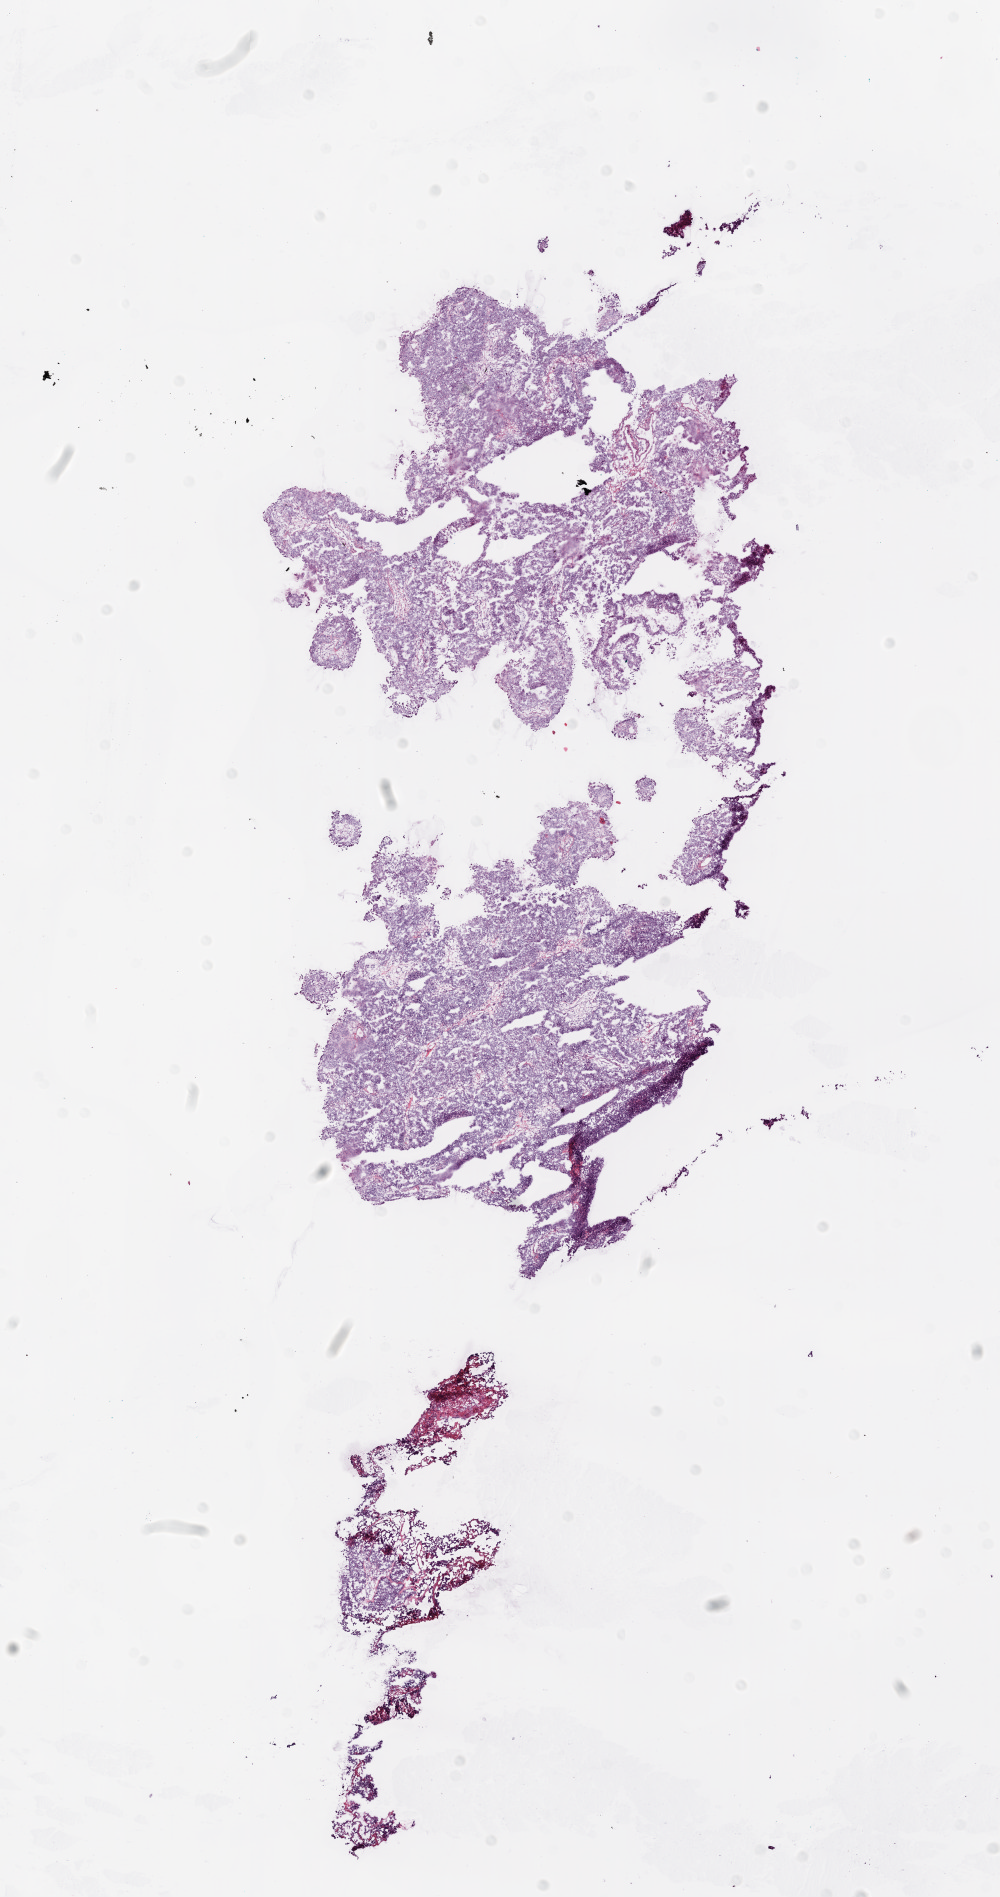
Digitized H&E-stained tissue section (whole slide) — a low-resolution overview of the entire scanned area, about 8.0 x 15.2 mm (slide scanned at 20x), frozen section from the top of the tissue portion, sample: primary tumour, ovary. Female, age 63 years at initial diagnosis. Histologic grade: G3 (poorly differentiated). Slide review estimates, as recorded: tumour cells 90%, tumour nuclei 95%, normal cells 0%, stromal cells 5%, necrosis 5%.
- pathologic diagnosis: Serous cystadenocarcinoma, NOS
- FIGO stage: IIIC